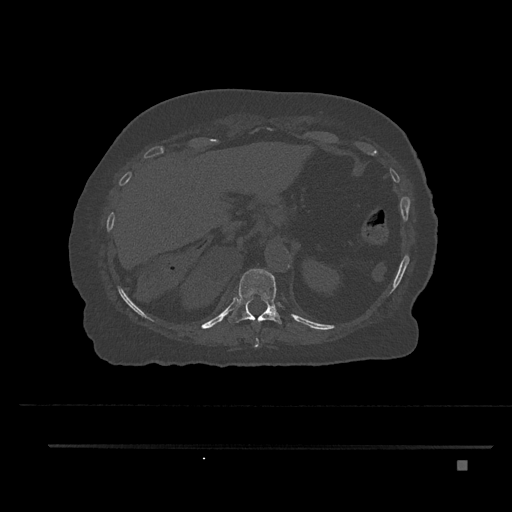
CT including the spine, one axial slice. Slice 315 of 797 in the series (ordered by position). Reconstruction kernel Br40s/3. 120 kVp. Bone window (W 1800 / L 400 HU). 0.5 mm slice thickness. 512 × 512 image matrix, field of view 437 × 437 mm. Female patient, age 76 years. From the clinical record (not read from this slice): primary cancer: lung; vertebrae with lytic lesions (as recorded): T11, L3.
Annotated regions visible in this slice (semi-automatic segmentation, software-assisted and operator-edited):
- T10 vertebra: box from (x=253, y=337) to (x=259, y=348) px
- T11 vertebra: (x=228, y=269)–(x=282, y=325)